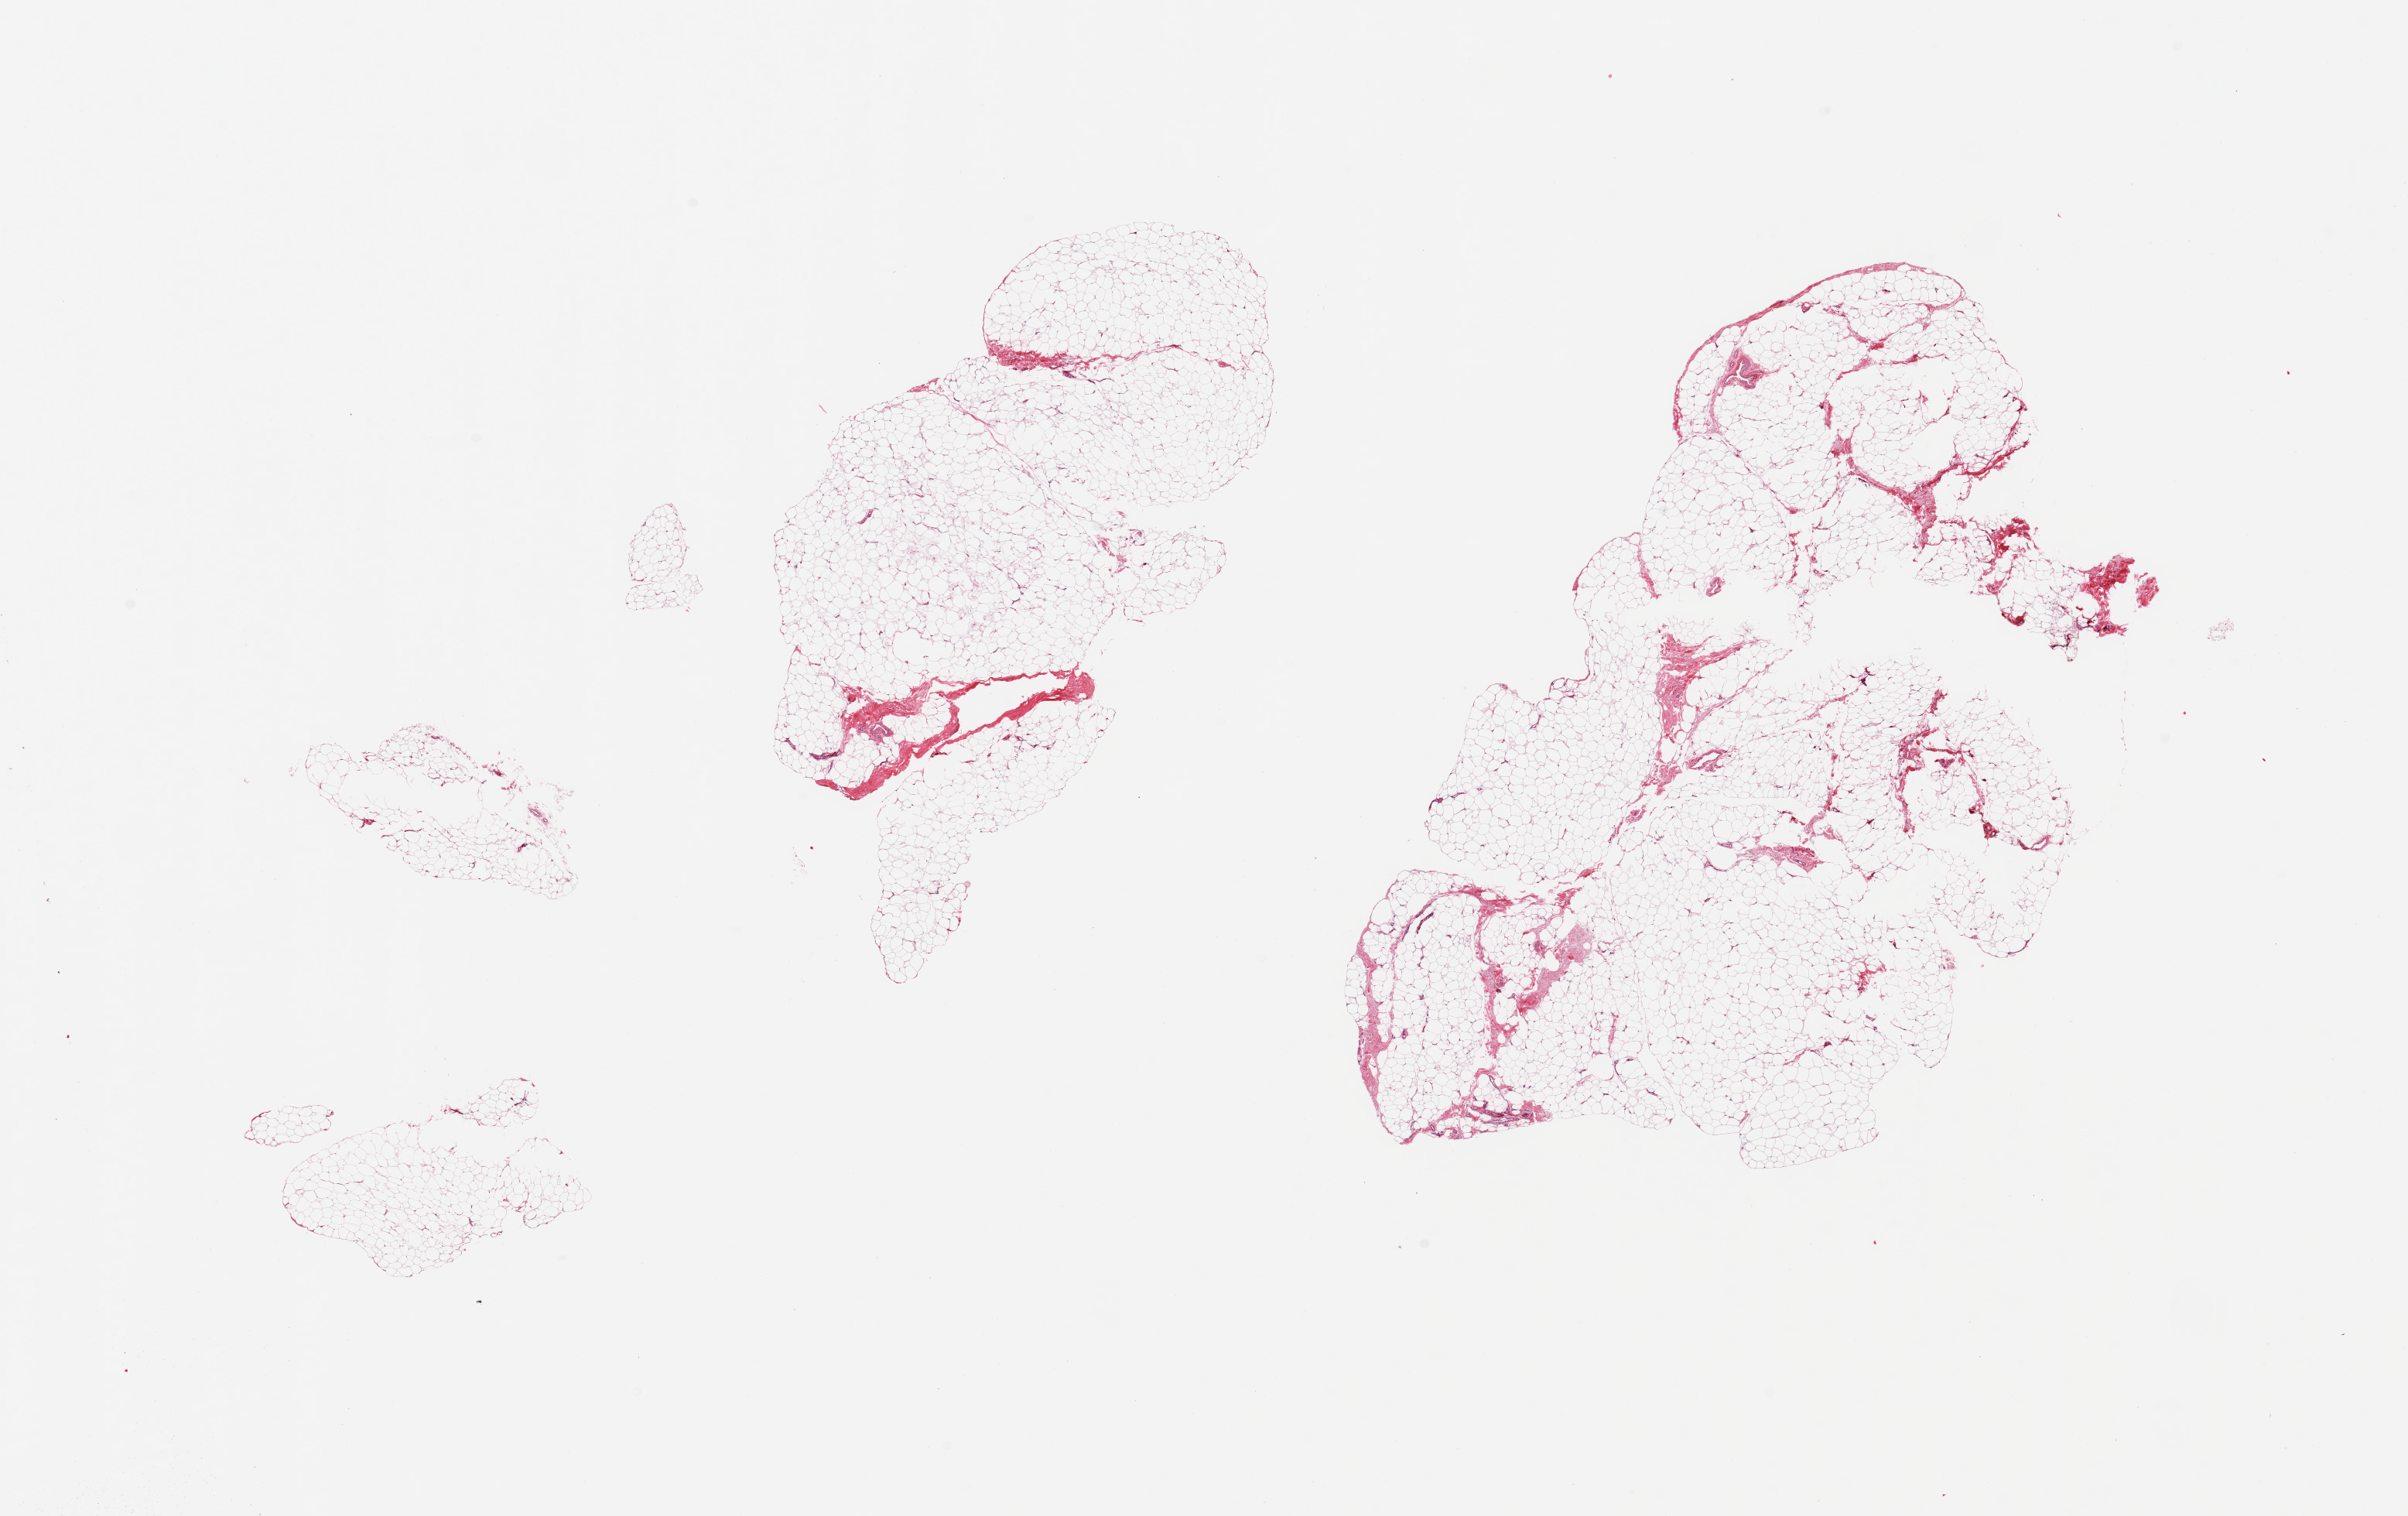
Digitized haematoxylin and eosin-stained section — a low-resolution overview of the entire scanned area, about 24.6 x 15.5 mm (from a 20x scan), PAXgene-fixed paraffin-embedded (PFPE) section, section of adipose tissue (target tissue), tissue donor sample. Male donor.
Reviewer comment on this tissue sample: 2 pieces, ~5% fascia.